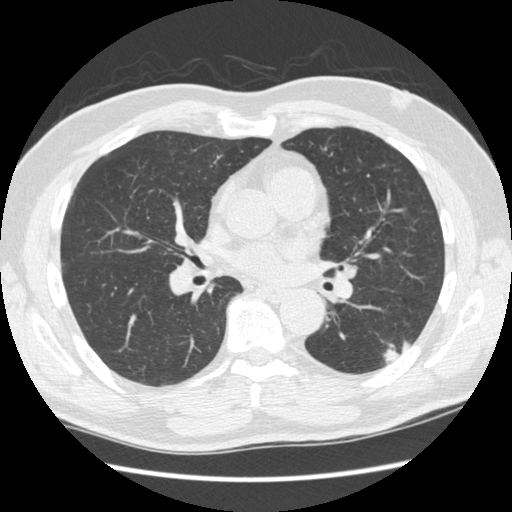
Low-dose screening chest CT, axial slice; baseline screening round; lung window (W 1500 / L -600 HU); 1.25 mm slice thickness; standard (soft-tissue) reconstruction kernel (STANDARD); slice 125 of 267 in the series; 512 × 512 image matrix. Male participant, aged 74 years at enrolment. Former smoker at enrolment.
Expert reader's lesion annotation, bounding box [x1, y1, x2, y2] px = [374, 324, 416, 371]. The screening reader recorded 3 non-calcified nodules or masses ≥4 mm on this exam (right upper lobe, right lower lobe, left upper lobe); which of them this box marks is not recorded. Participant outcome: lung cancer diagnosed 384 days after this screen — squamous cell carcinoma, NOS, left lower lobe, well differentiated (G1), stage IA (AJCC 6th edition), 28 mm at pathology.